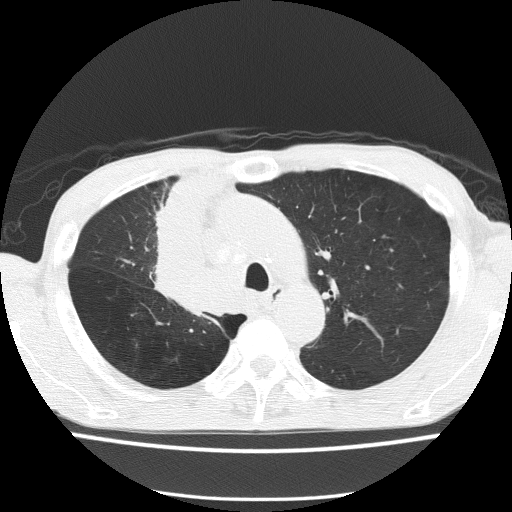
Chest CT (low-dose screening protocol), one axial image. Baseline screening round. Lung window (W 1500 / L -600 HU). 2 mm slice thickness. Slice 44 of 150 in the series. 512 × 512 image matrix, field of view 336 × 336 mm. Male participant, aged 59 years at enrolment. Former smoker at enrolment.
• Expert-annotated lung lesion, box from (x=135, y=233) to (x=236, y=325) px.
• The screening reader recorded 5 non-calcified nodules or masses ≥4 mm on this exam (left upper lobe, left upper lobe, left upper lobe, right middle lobe, right lower lobe); which of them this box marks is not recorded.
• Official screen result: positive, change unspecified: nodule(s) >= 4 mm or enlarging nodule(s), mass(es), or other non-specific abnormalities suspicious for lung cancer.
• Later outcome: lung cancer diagnosed 72 days after this screen — squamous cell carcinoma, NOS, right upper lobe, moderately differentiated (G2), stage IV (AJCC 6th edition).